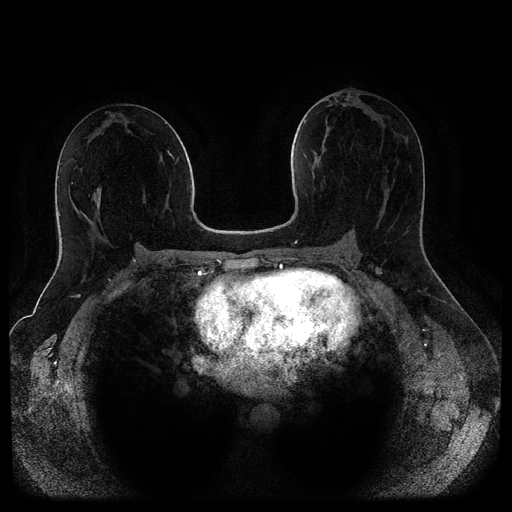
Breast MRI (dynamic contrast-enhanced, multi-phase), one axial slice; slice 50 of 116 in the series (ordered by position); dynamic contrast-enhanced series, time point 2 of 5 at this slice position (early post-contrast); 1.5 T; TE 2.6 ms, TR 5.3 ms; 2 mm slice thickness; 512 × 512 image matrix. Female patient, age 44 years.
Structures marked on this image (semi-automatically segmented with operator editing):
- breast lesion (labelled benign in the annotation): bounding box (x1, y1, x2, y2) in pixels: (93, 189, 101, 211)